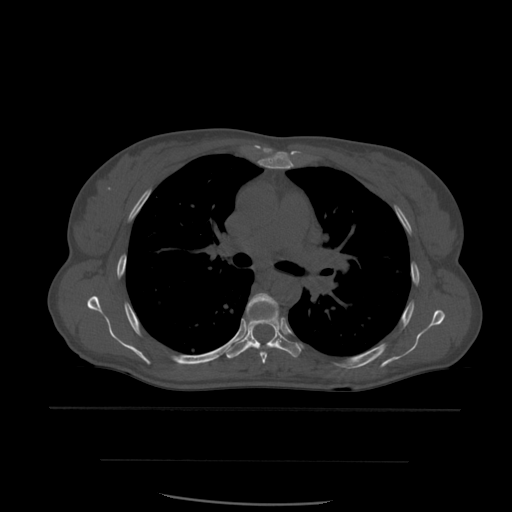
CT including the spine, one axial slice; position 399 of 574 along the scan axis; bone window (W 1800 / L 400 HU); 1.25 mm slice thickness; 512 × 512 image matrix, field of view 392 × 392 mm. Patient age 48 years. From the clinical record (not read from this slice): primary cancer: lung; vertebrae with lytic lesions (as recorded): T11.
Outlined on this slice (semi-automatically segmented with operator editing):
- T5 vertebra: bounding box (x1, y1, x2, y2) in pixels: (247, 293, 280, 364)
- T6 vertebra: (227, 315, 302, 359)